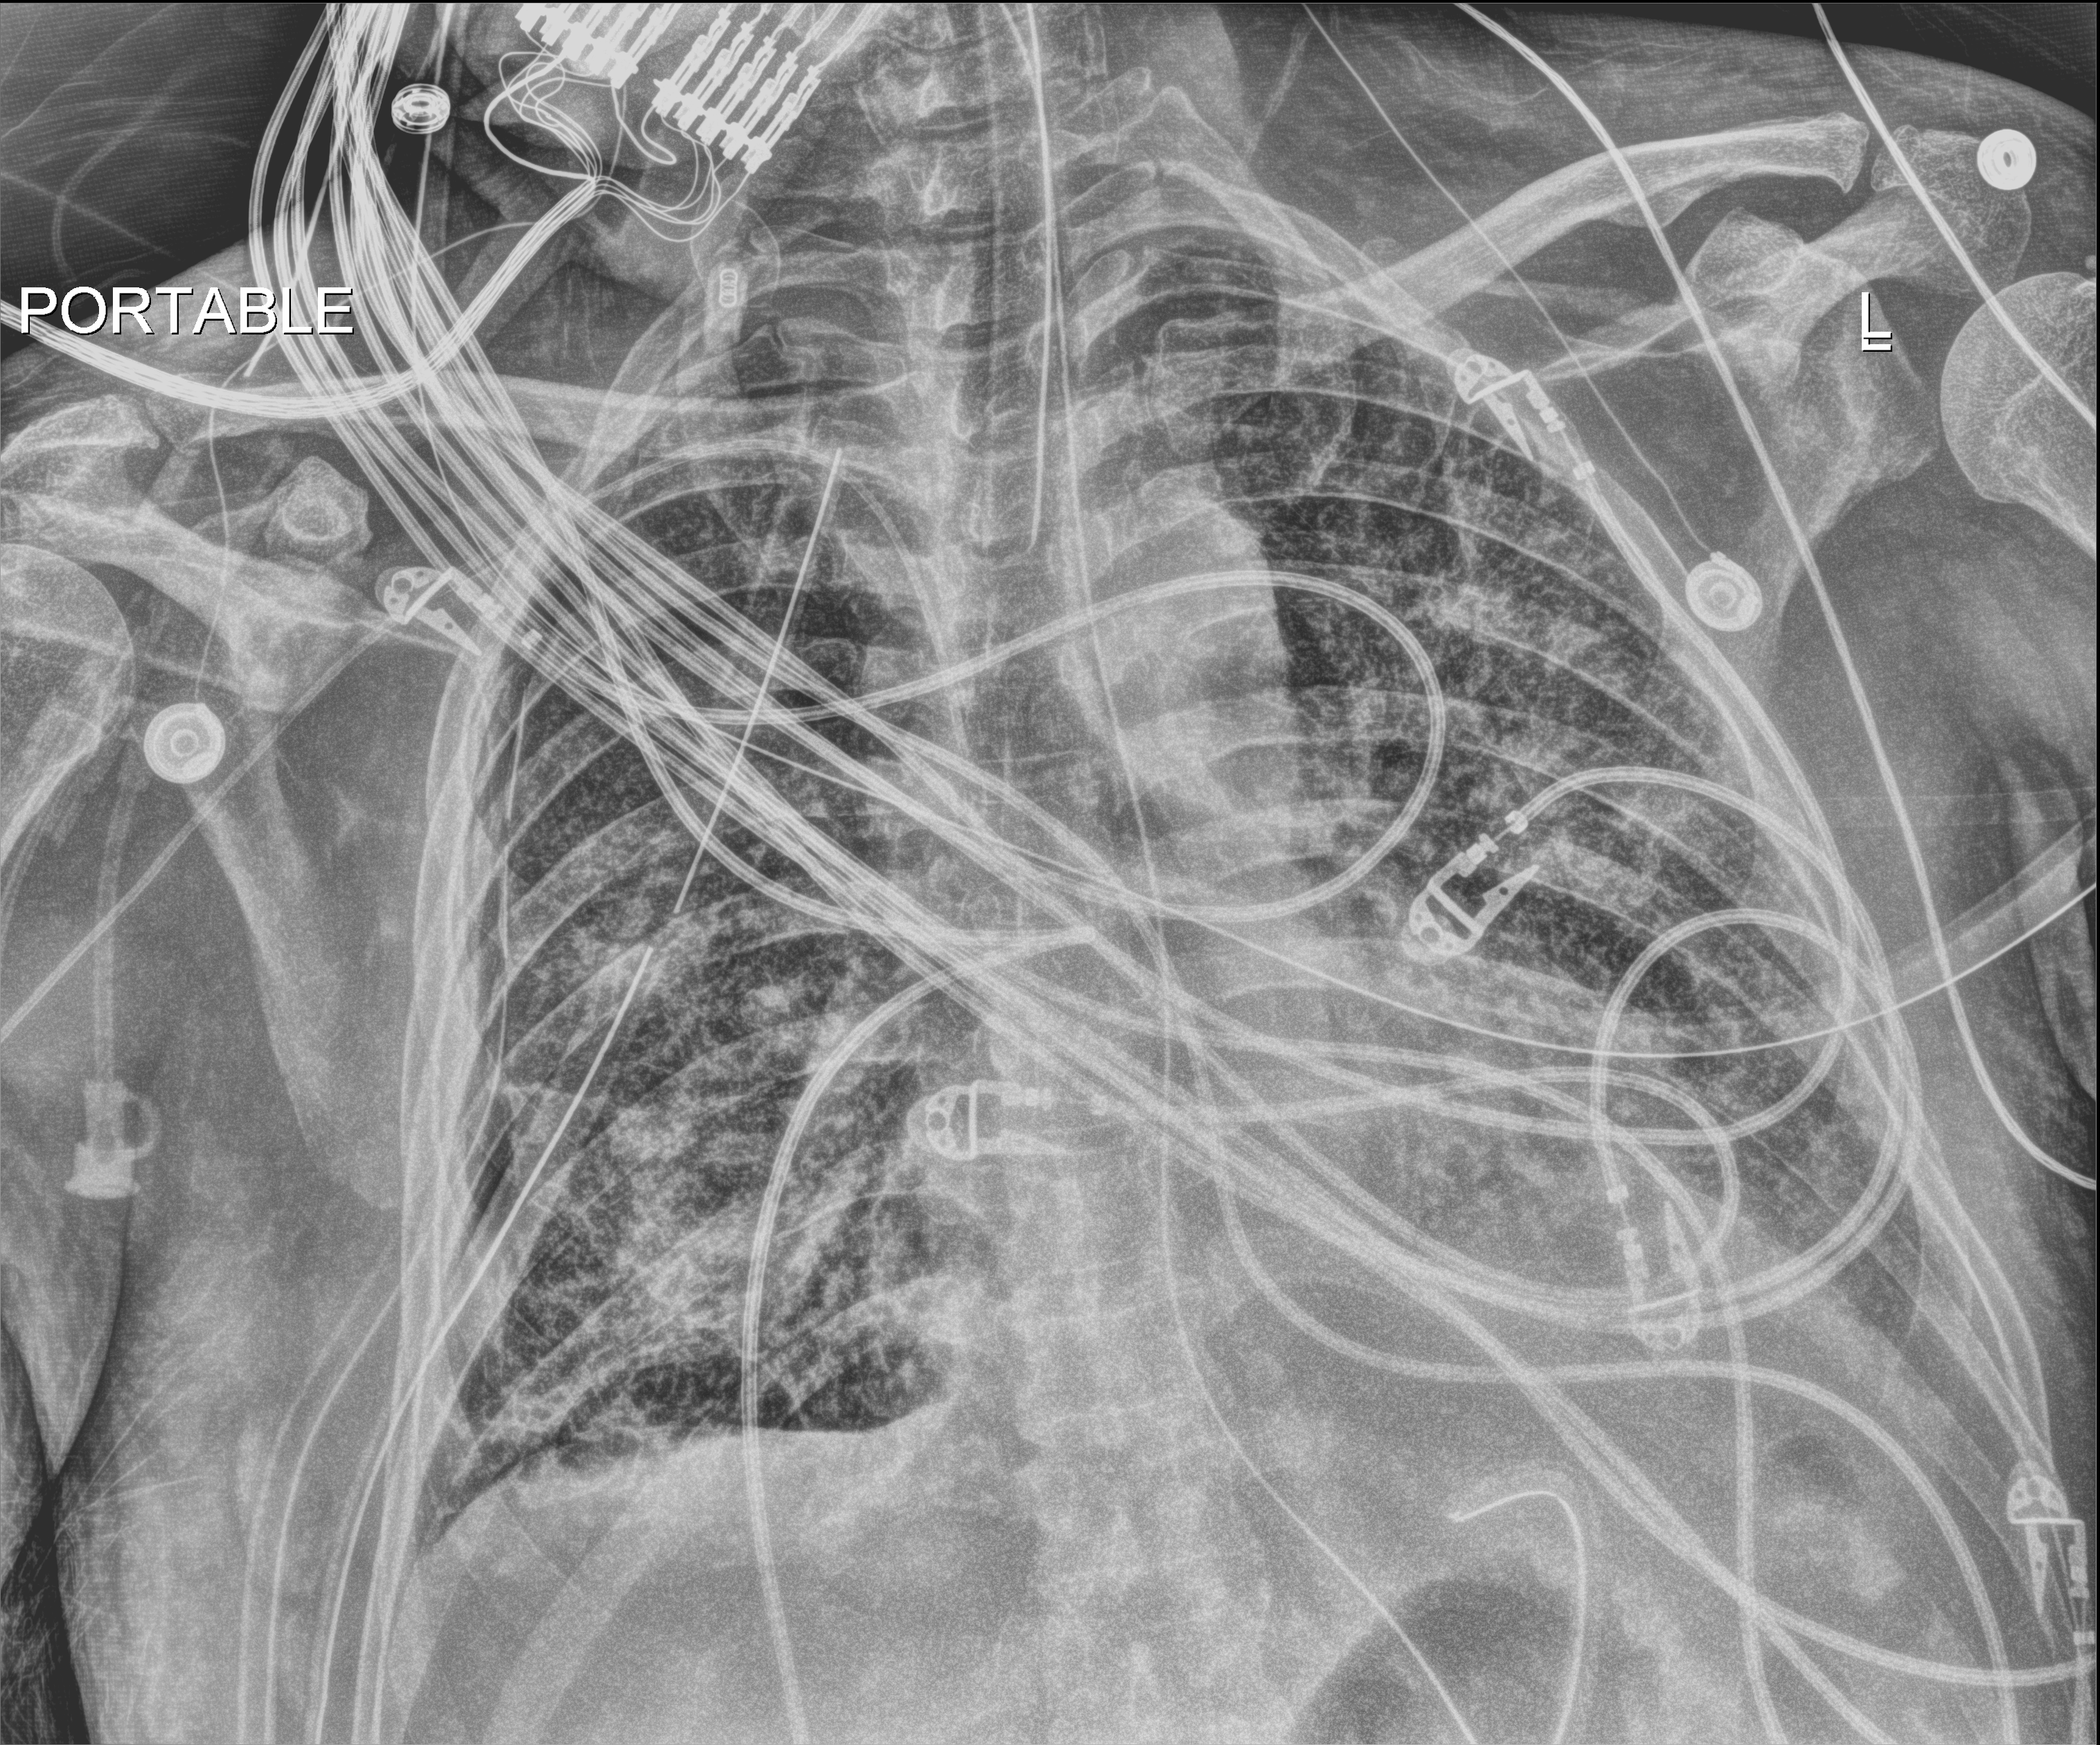
Portable chest radiograph; anteroposterior (AP) projection. Male patient hospitalised with COVID-19, age 60–74 years.
Admission-level facts for this patient (not findings on this image; timing relative to this image not recorded): mechanically ventilated during this hospital stay: yes; length of hospital stay: 37 days.